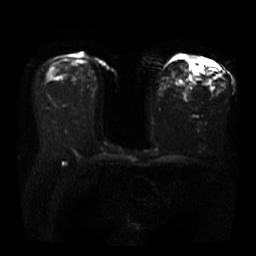
Breast MRI, one axial slice. Slice 20 of 40 in the series (ordered by position). Diffusion-weighted series; image 2 of 4 stored at this slice position (different b-values; order by instance number). 3 T. 5 mm slice thickness. 256 × 256 image matrix, field of view 360 × 360 mm. Female patient.
Outlined on this slice (manually delineated by an expert):
- tumour on diffusion-weighted imaging: bounding box (x1, y1, x2, y2) in pixels: (190, 60, 200, 73)